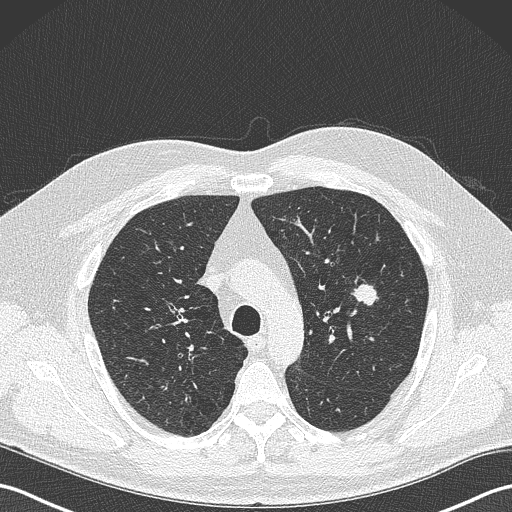
Low-dose screening chest CT, one axial slice. Slice 247 of 343 in the series (ordered by position). Lung window (W 1500 / L -600 HU). 1 mm slice thickness. 512 × 512 image matrix, field of view 350 × 350 mm.
Outlined on this slice (expert manual segmentation):
- lesion 1 (tumor, upper lobe of left lung): bounding box <351,280,379,306> (left, top, right, bottom; pixels)